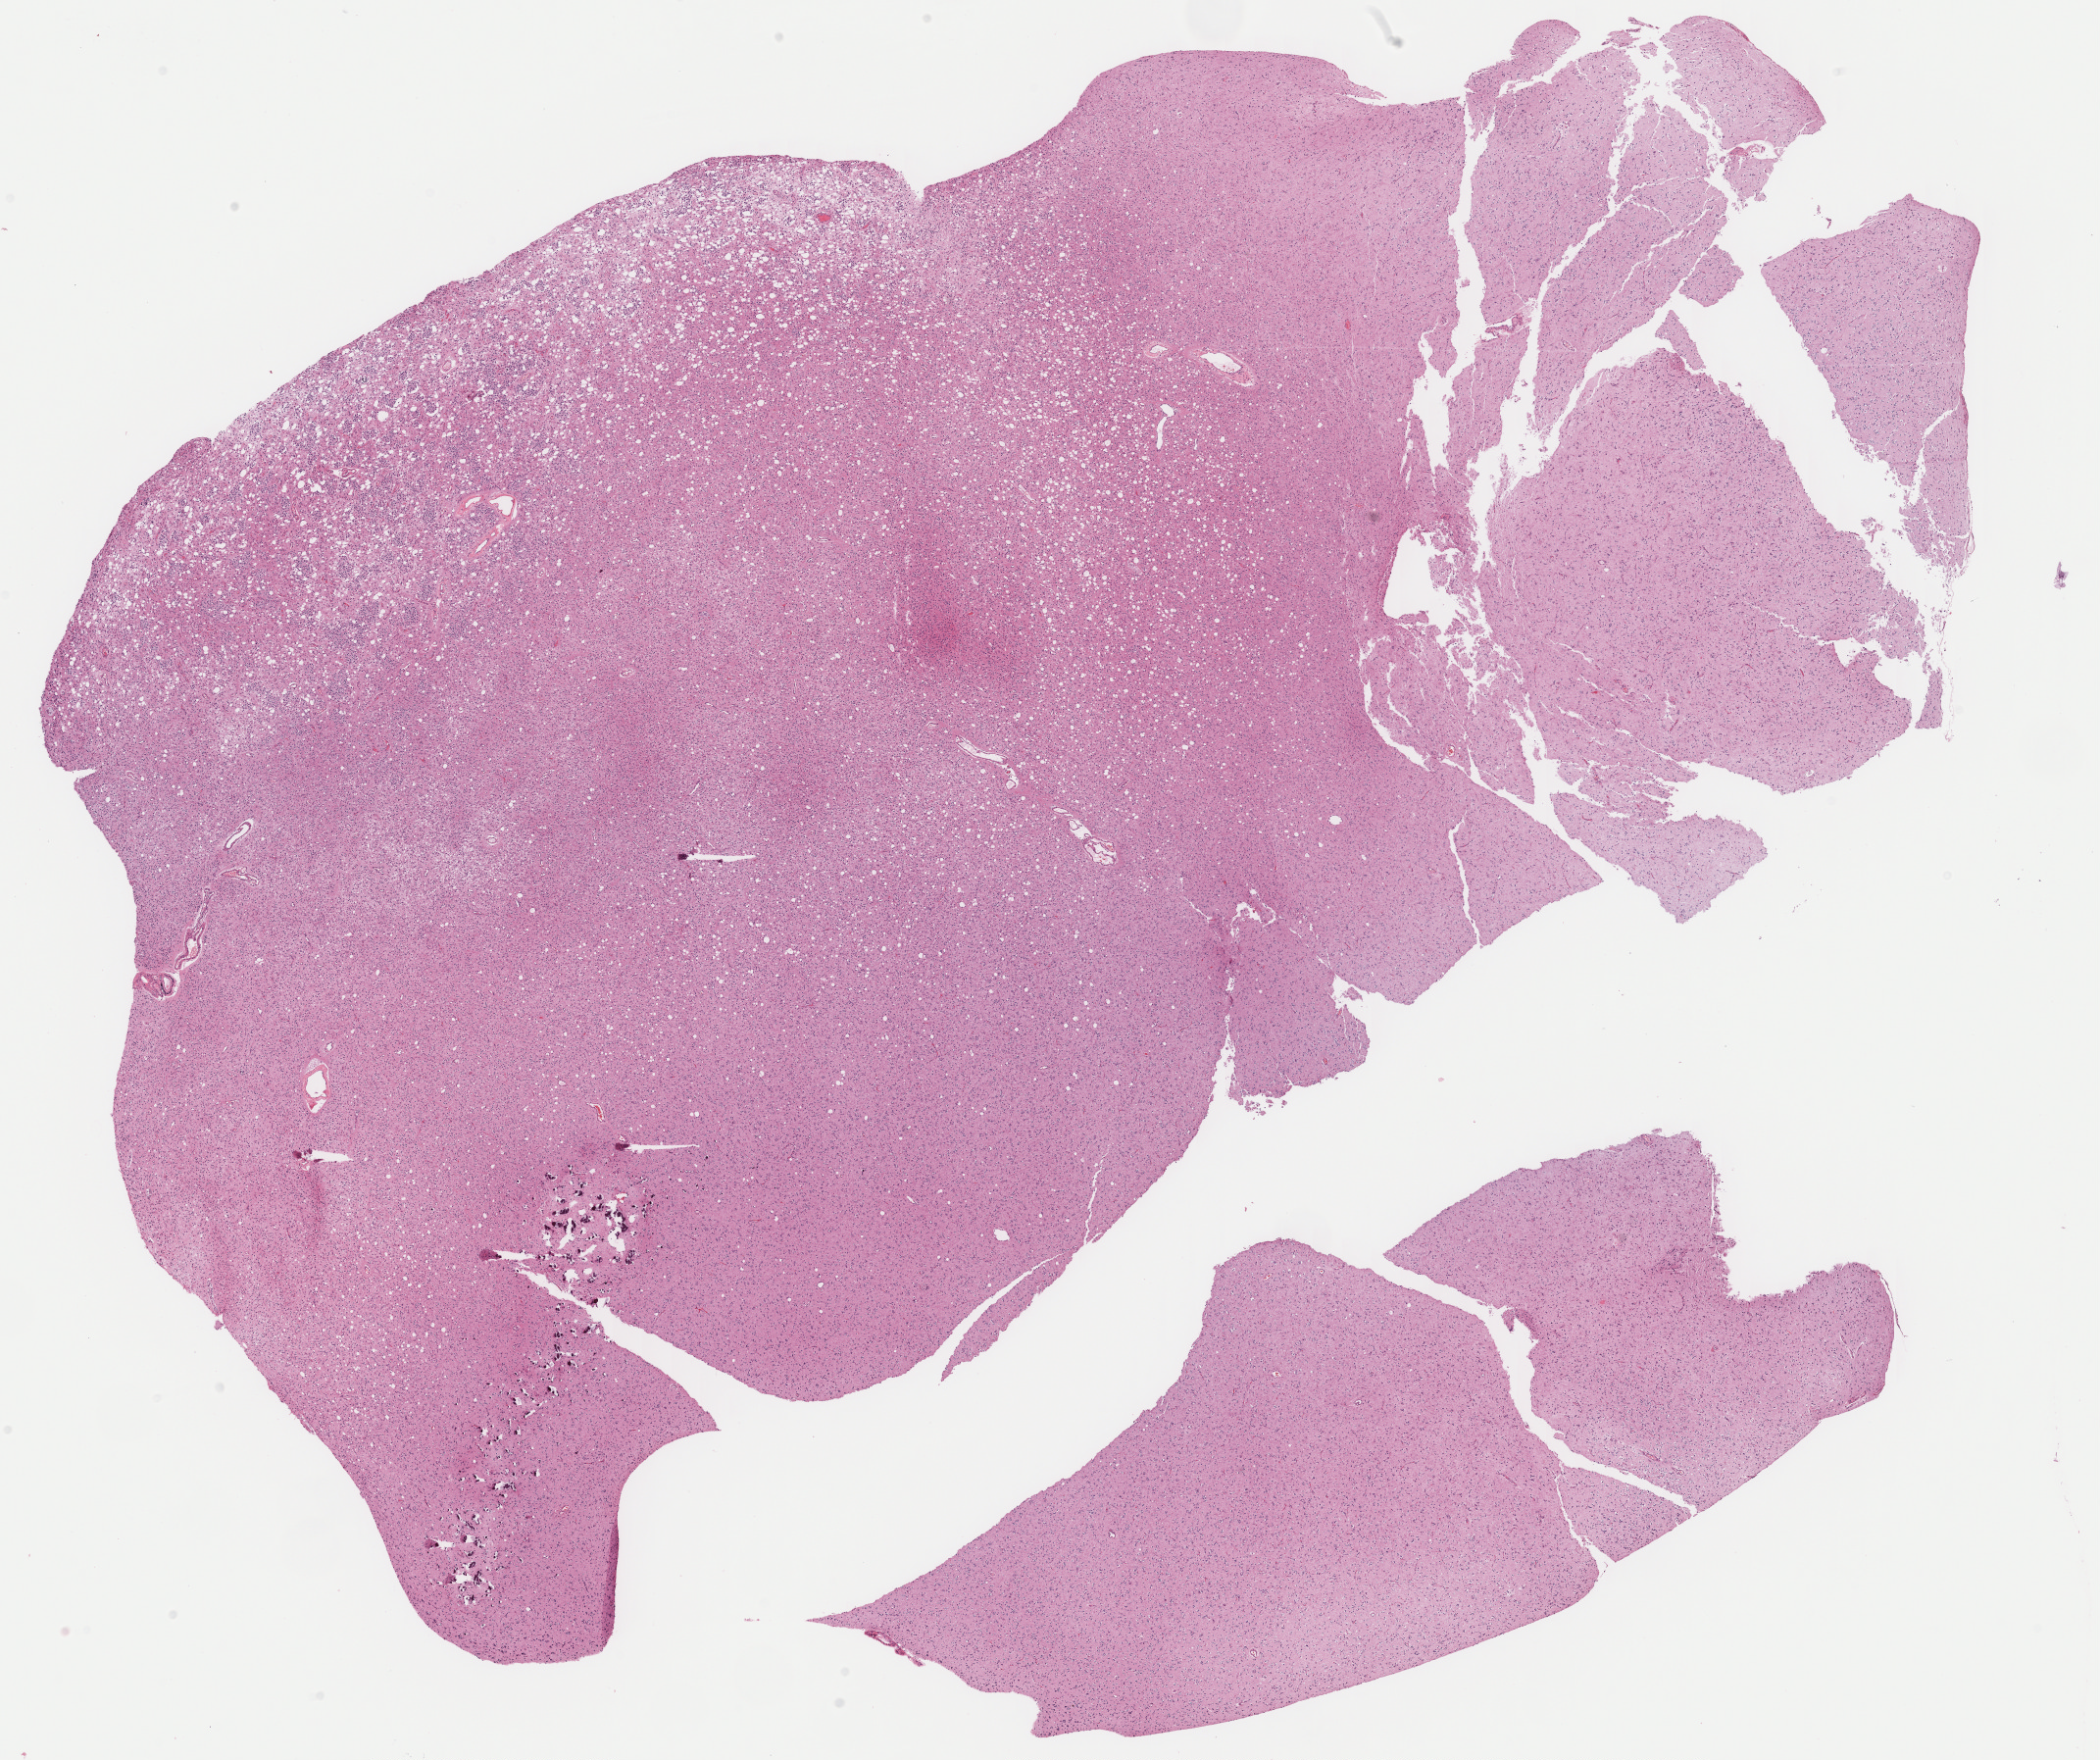
Digitized H&E-stained tissue section (whole slide), a low-resolution overview of the entire scanned area, about 16.9 x 14.1 mm (acquisition: 40x scan); FFPE section; sample: primary tumour, brain. Female patient; age at initial diagnosis 53 years. Histologic grade: G2 (moderately differentiated).
* histologic diagnosis: Mixed glioma (frontal lobe)